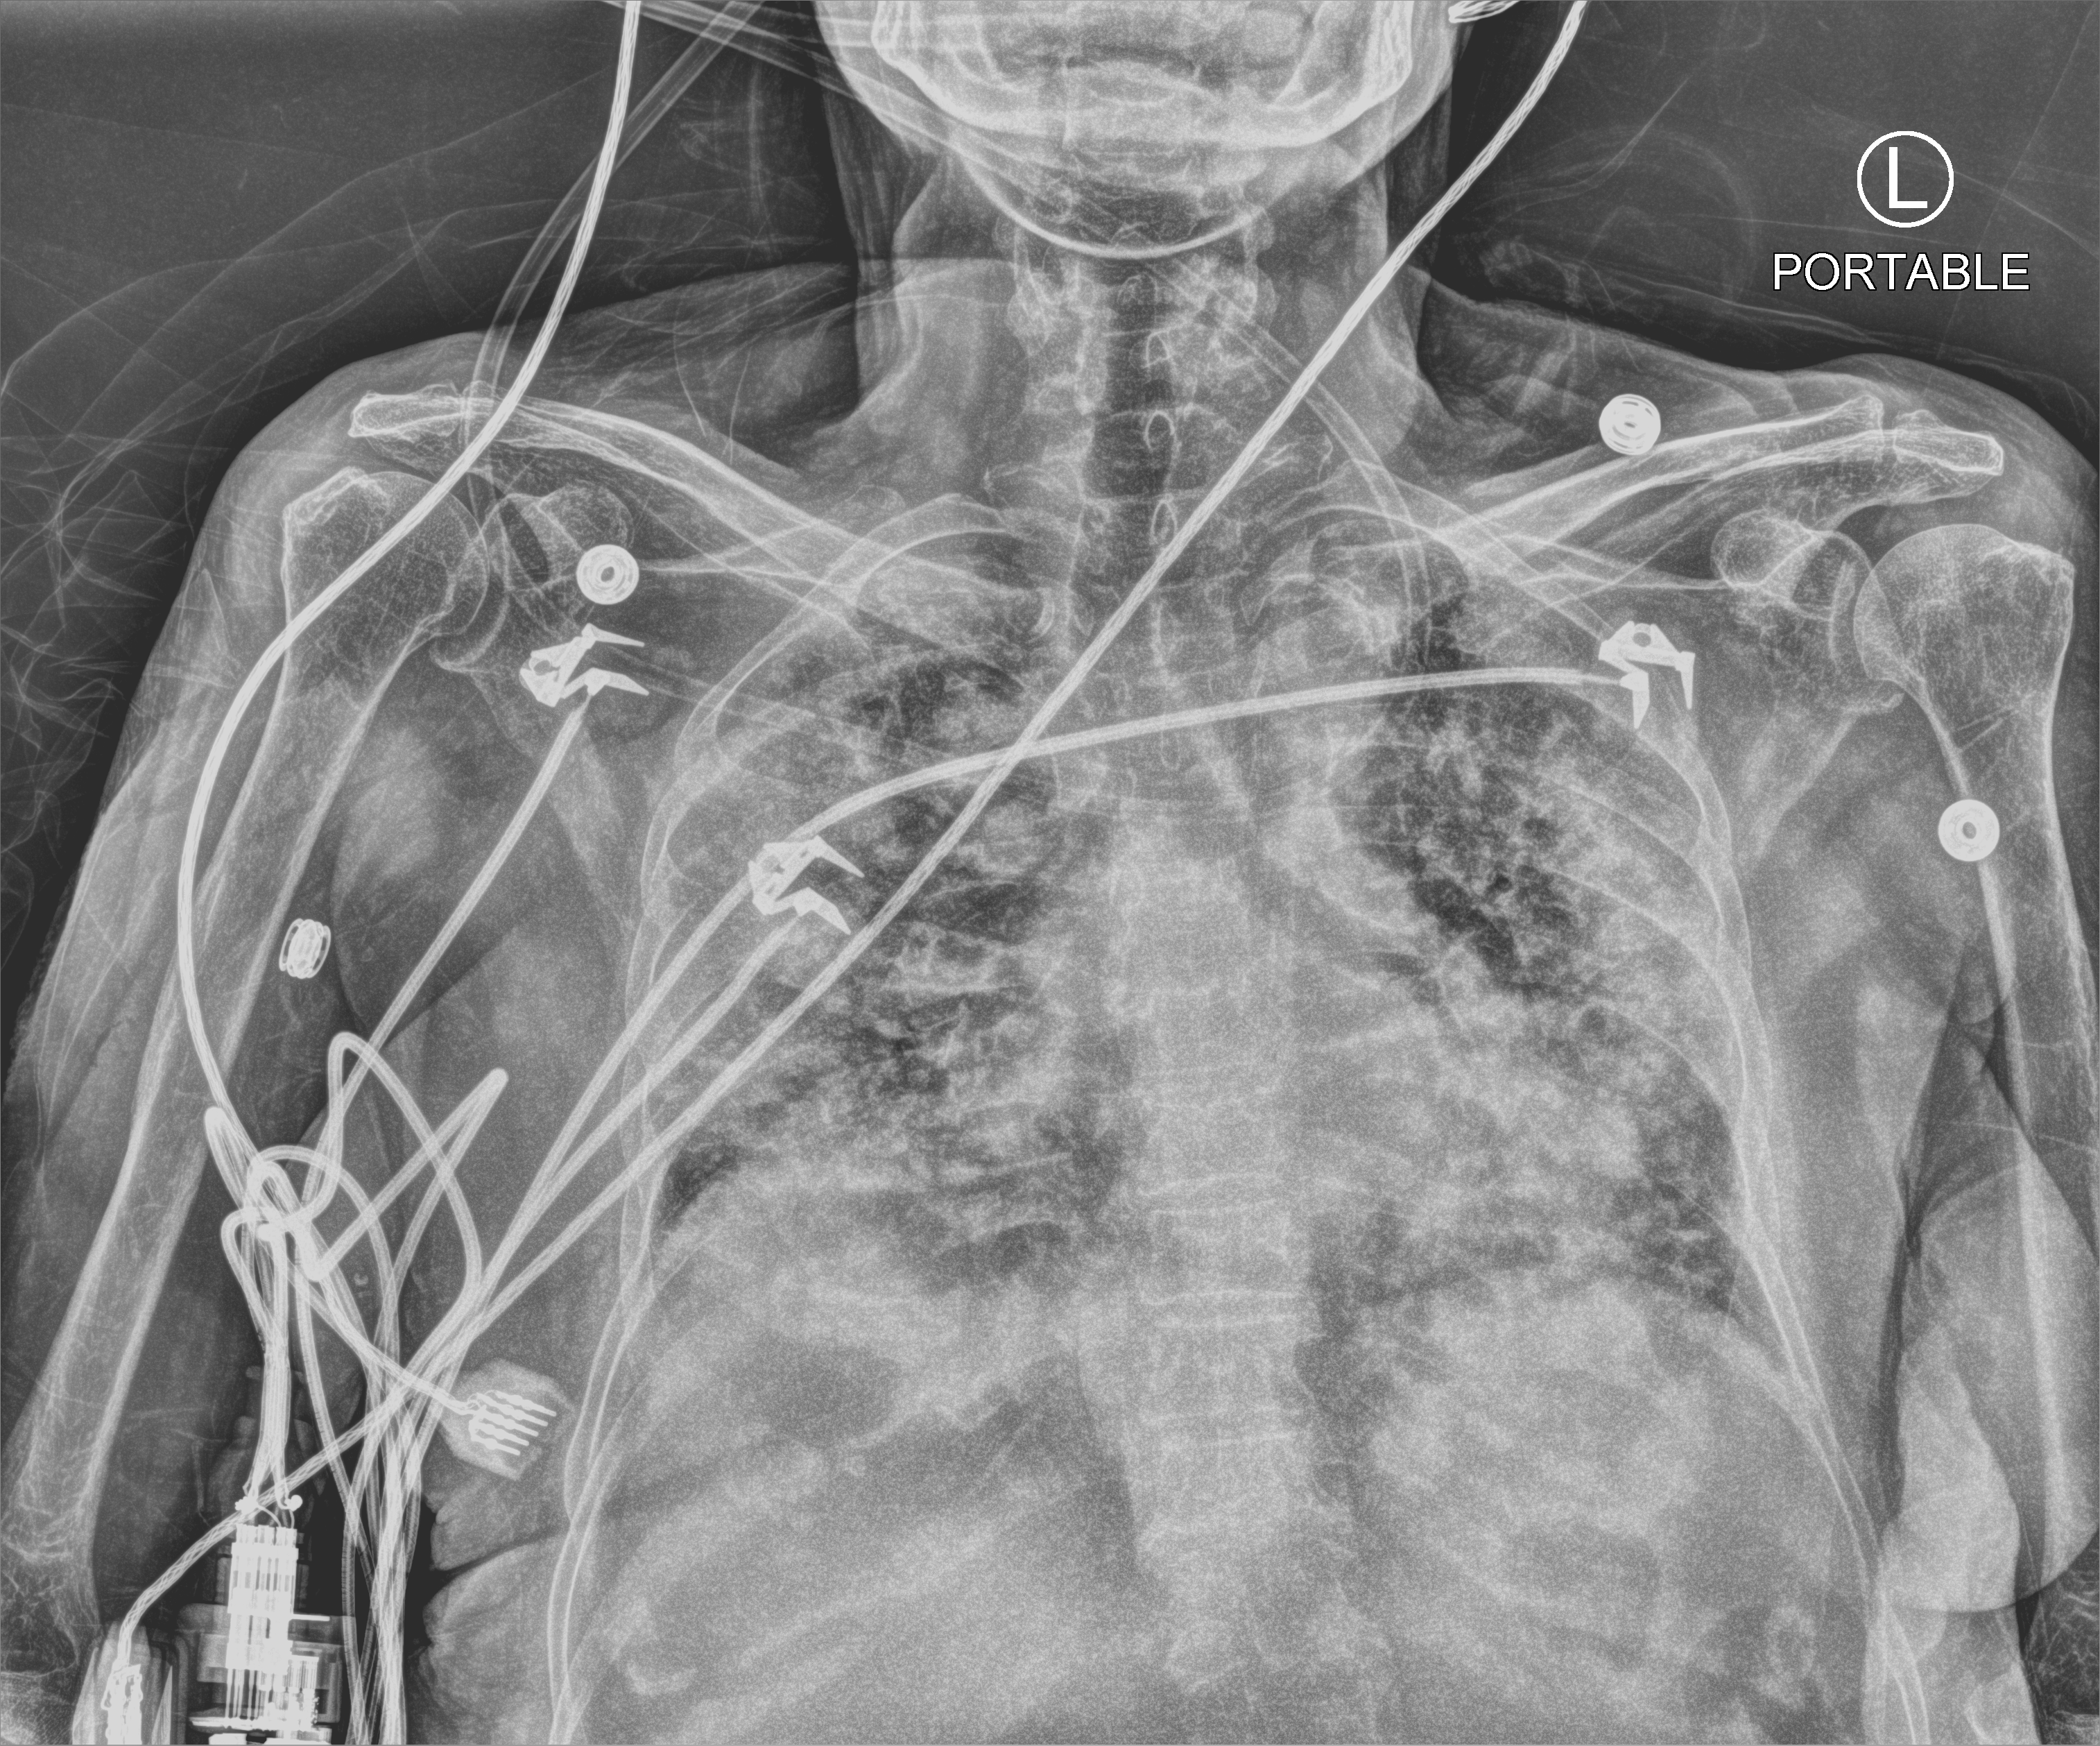
Bedside chest radiograph (computed radiography), anteroposterior (AP) projection. Female patient hospitalised with COVID-19, age 75–90 years.
Admission-level facts for this patient (not findings on this image; timing relative to this image not recorded):
- admitted to intensive care during this hospital stay: no